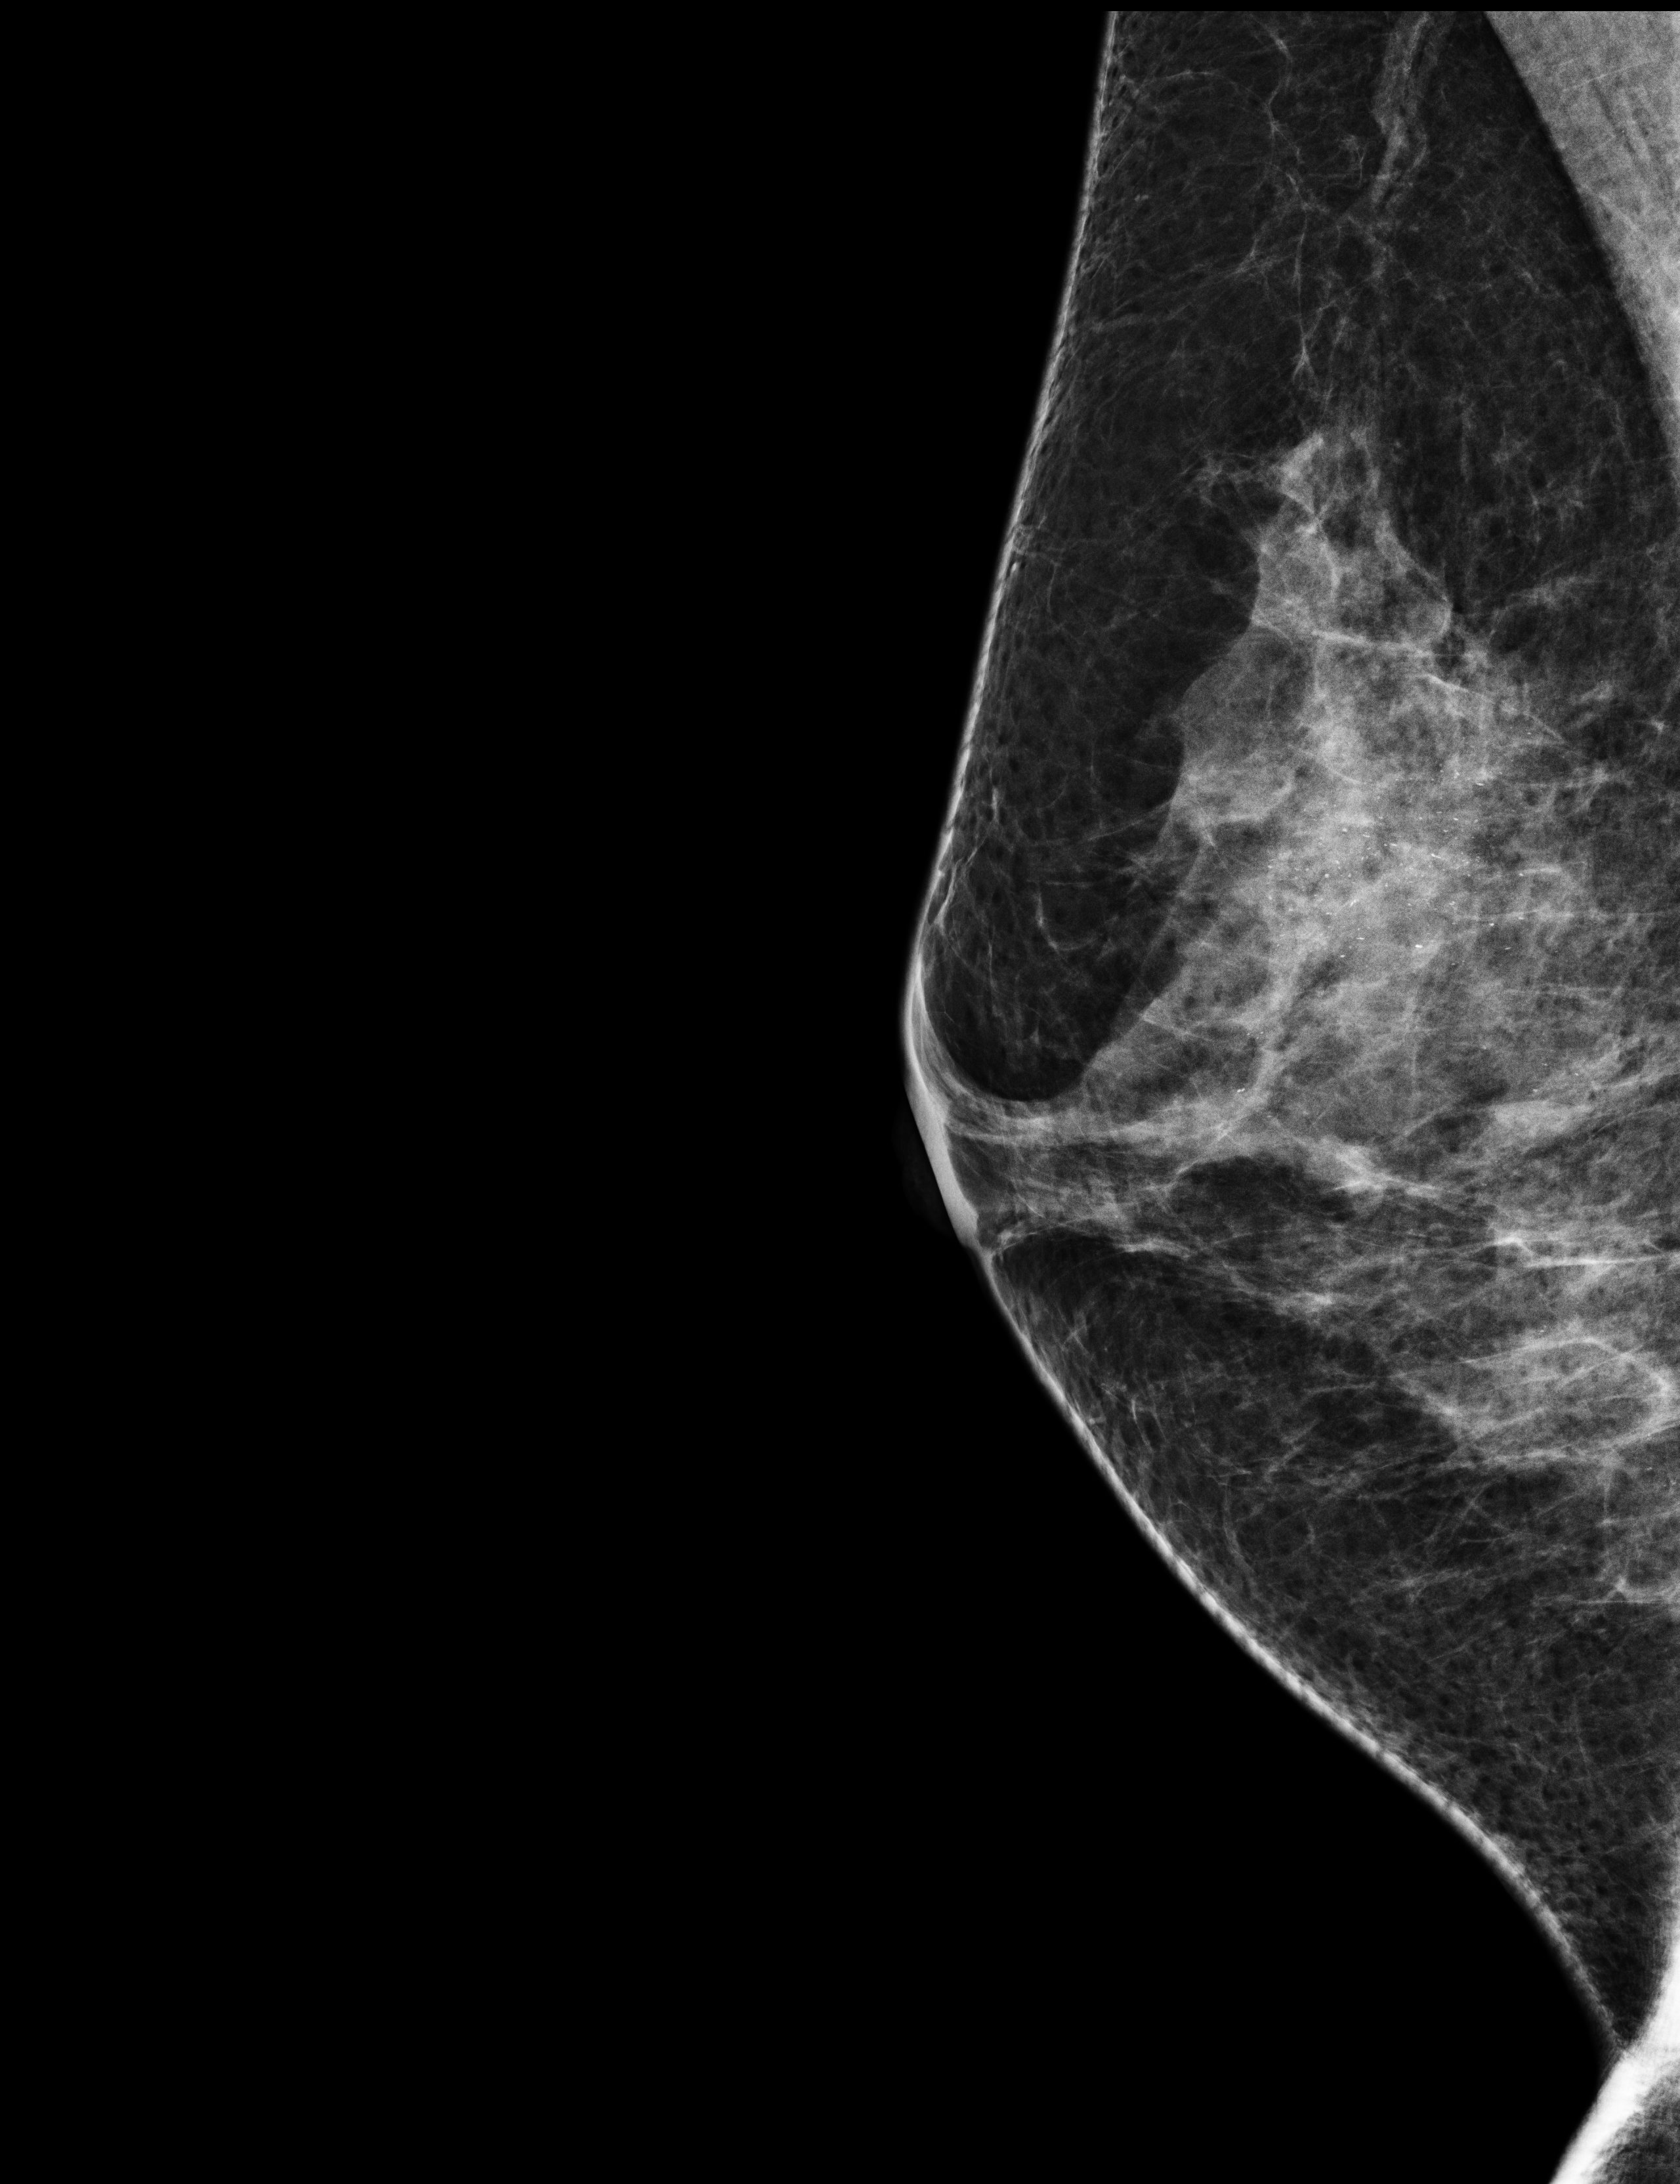
Full-field digital mammogram (FFDM); right breast; ML view; screening examination; compressed breast thickness 55 mm. Female patient, age 48 years.
Final BI-RADS category for the screening round (tomosynthesis exam, both breasts): category 4.